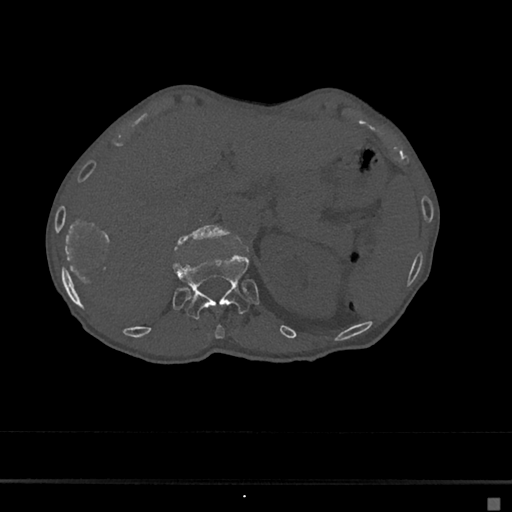
CT including the spine, one axial slice. Position 124 of 797 along the scan axis. Reconstruction kernel Br40s/3. 120 kVp. Bone window (W 1800 / L 400 HU). 512 × 512 image matrix, field of view 360 × 360 mm. Female patient, age 68 years. From the clinical record (not read from this slice): primary cancer: renal.
Outlined on this slice (semi-automatic segmentation, software-assisted and operator-edited):
- L1 vertebra: box from (x=178, y=225) to (x=227, y=244) px
- T11 vertebra: (x=214, y=324)–(x=225, y=339)
- T12 vertebra: (x=173, y=253)–(x=250, y=320)